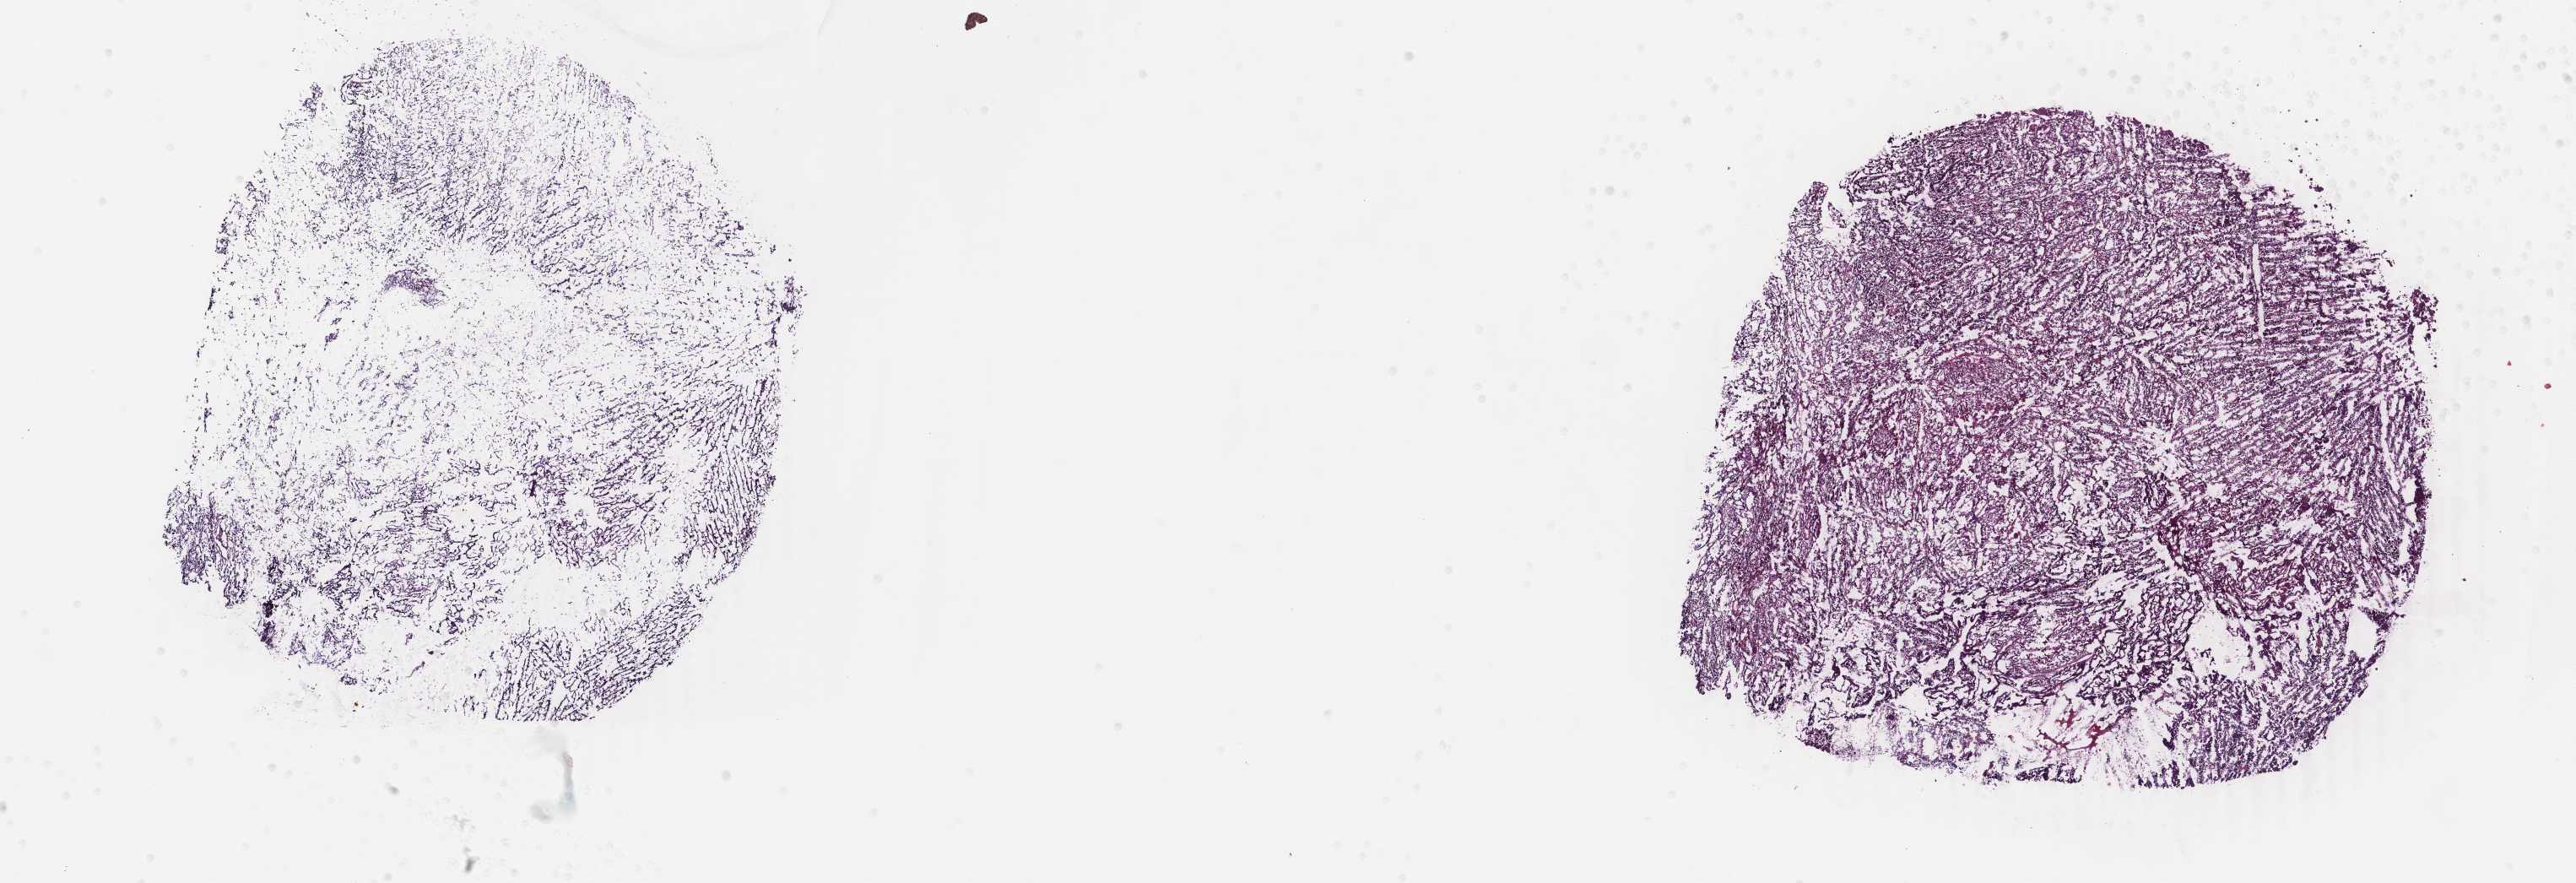
Digitized H&E tissue section (whole slide), shown as a low-resolution overview of the whole scanned area (about 24.3 x 8.3 mm, acquisition: 40x scan); frozen section; uterus, primary tumour sample. Female, age 59 years at initial diagnosis. Histologic grade: G2 (moderately differentiated). Pathologist review of this section (percent, as recorded): tumour cells 100%, tumour nuclei 85%, normal cells 0%, stromal cells 0%, necrosis 0%. Infiltration values recorded for this section: lymphocyte infiltration 0%, monocyte infiltration 0%, neutrophil infiltration 0%.
Lymph nodes positive (case pathology): 0 of 33 examined. FIGO stage: IA. Histologic diagnosis: Endometrioid adenocarcinoma, NOS (endometrium).